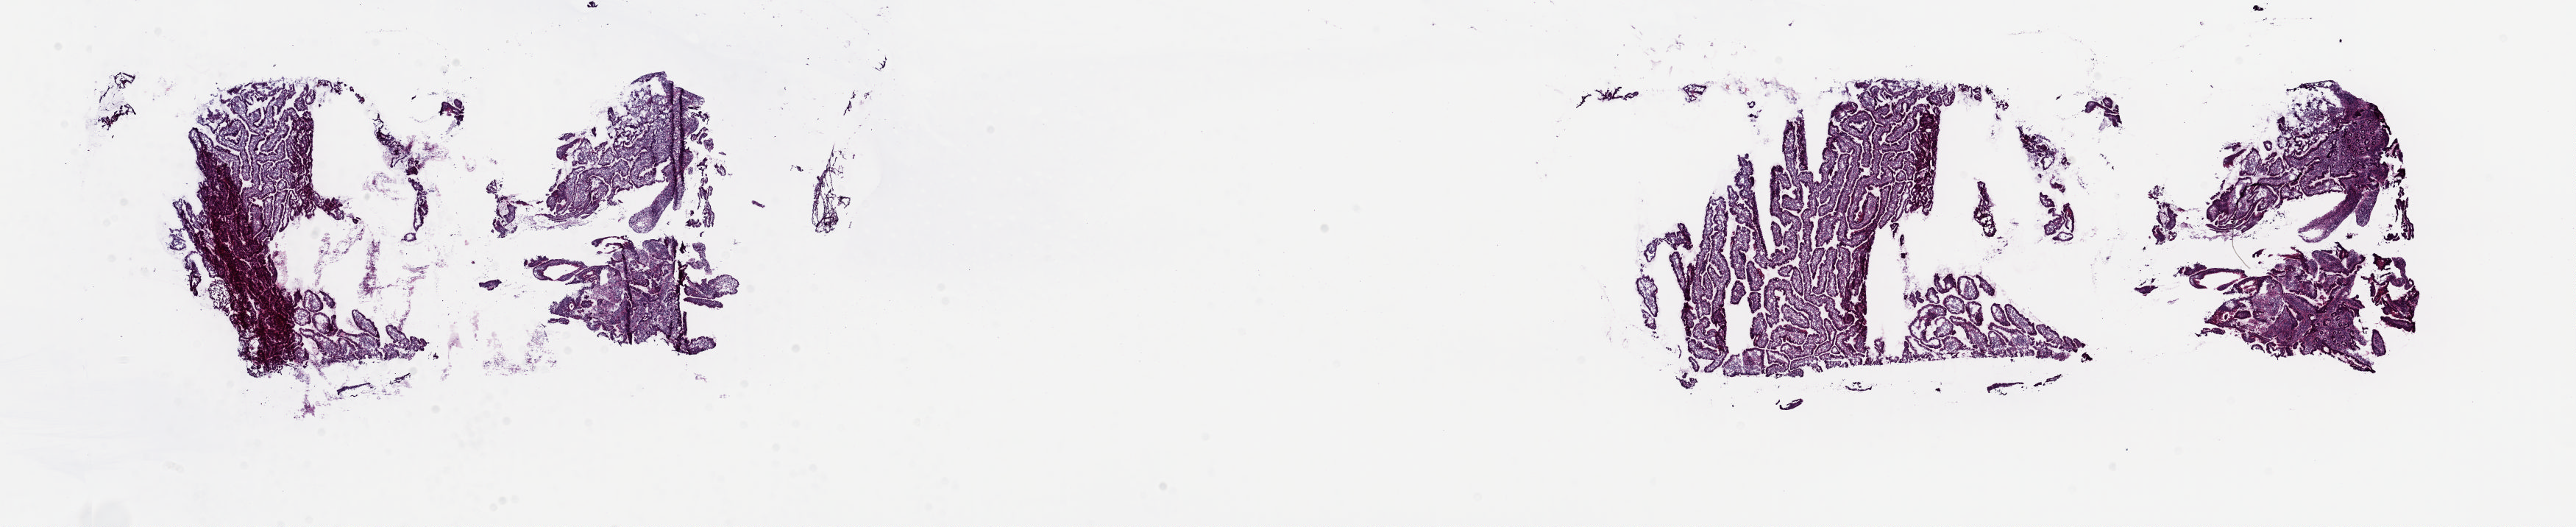
Hematoxylin and eosin (H&E) stained whole-slide image, a low-resolution overview of the entire scanned area, about 27.8 x 5.7 mm (slide scanned at 20x); frozen section from the top of the tissue portion; solid tissue normal (non-tumour tissue) sample from the bile duct. Patient sex: female. Pathologist review of this section (percent, as recorded): tumour cells 0%, tumour nuclei 0%, normal cells 100%, stromal cells 0%, necrosis 0%. Inflammatory infiltration, as recorded: lymphocyte infiltration 3%, monocyte infiltration 0%, neutrophil infiltration 0%.
* this section: solid tissue normal (non-tumour) sample from the same patient
* patient diagnosis: Cholangiocarcinoma (extrahepatic bile duct)